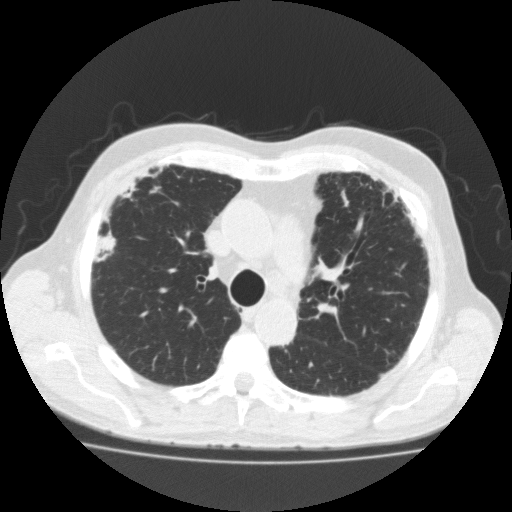
Low-dose screening chest CT, one axial slice; position 131 of 188 along the scan axis; reconstruction kernel FC10; 120 kVp; lung window (W 1500 / L -600 HU); 512 × 512 image matrix, field of view 391 × 391 mm.
Structures marked on this image (manually delineated by an expert):
- lesion 1 (tumor, upper lobe of right lung): bounding box <100,234,115,251> (left, top, right, bottom; pixels)